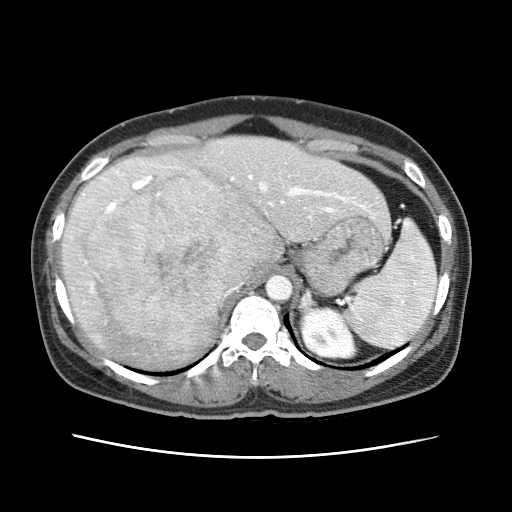
Contrast-enhanced abdominal CT (liver protocol), one axial slice. Soft-tissue window (W 400 / L 40 HU). 2.5 mm slice thickness. 512 × 512 image matrix, field of view 340 × 340 mm. From the clinical record (not read from this slice): diagnosis: hepatocellular carcinoma (patient treated with transarterial chemoembolisation; whether this scan precedes or follows treatment is not stated here); TNM stage (as recorded): Stage-I; Child-Pugh class: A; tumour differentiation: moderately differentiated; tumour nodularity: uninodular.
Annotated regions visible in this slice (semi-automatic segmentation, software-assisted and operator-edited):
- abdominal aorta: box from (x=266, y=275) to (x=294, y=301) px
- liver parenchyma outside the tumour (the mass and vessels are separate outlines, so this box may not span the whole liver): (x=62, y=136)–(x=382, y=366)
- mass: (x=91, y=179)–(x=279, y=349)
- liver vessels: (x=71, y=162)–(x=366, y=292)